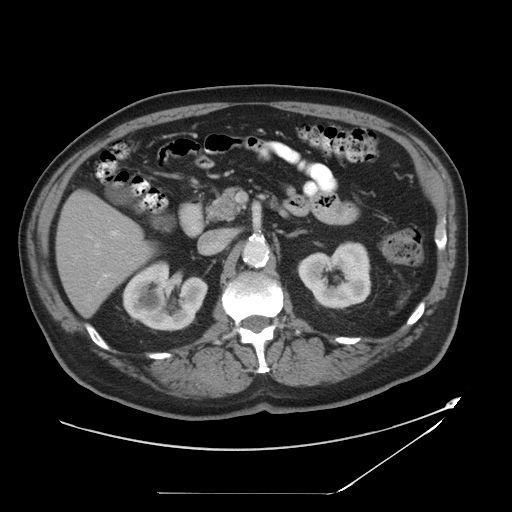
Contrast-enhanced abdominal CT, one axial slice; slice 21 of 49 in the series (ordered by position); reconstruction kernel STANDARD; 120 kVp; soft-tissue window (W 400 / L 40 HU); 5 mm slice thickness; 512 × 512 image matrix. Male patient, age 72 years. Case-level facts recorded for this patient, not image findings: diagnosis: colorectal cancer liver metastases, imaged before liver resection; multiple liver metastases: no; largest metastasis: 2.5 cm; disease in both lobes: no.
Annotated regions visible in this slice (manually delineated by an expert):
- hepatic veins: bounding box <86,234,102,248> (left, top, right, bottom; pixels)
- liver: <58,191,153,316>
- planned liver remnant (the part of the liver to remain after resection): <58,191,153,316>
- portal vein (with intrahepatic branches): <103,230,120,278>